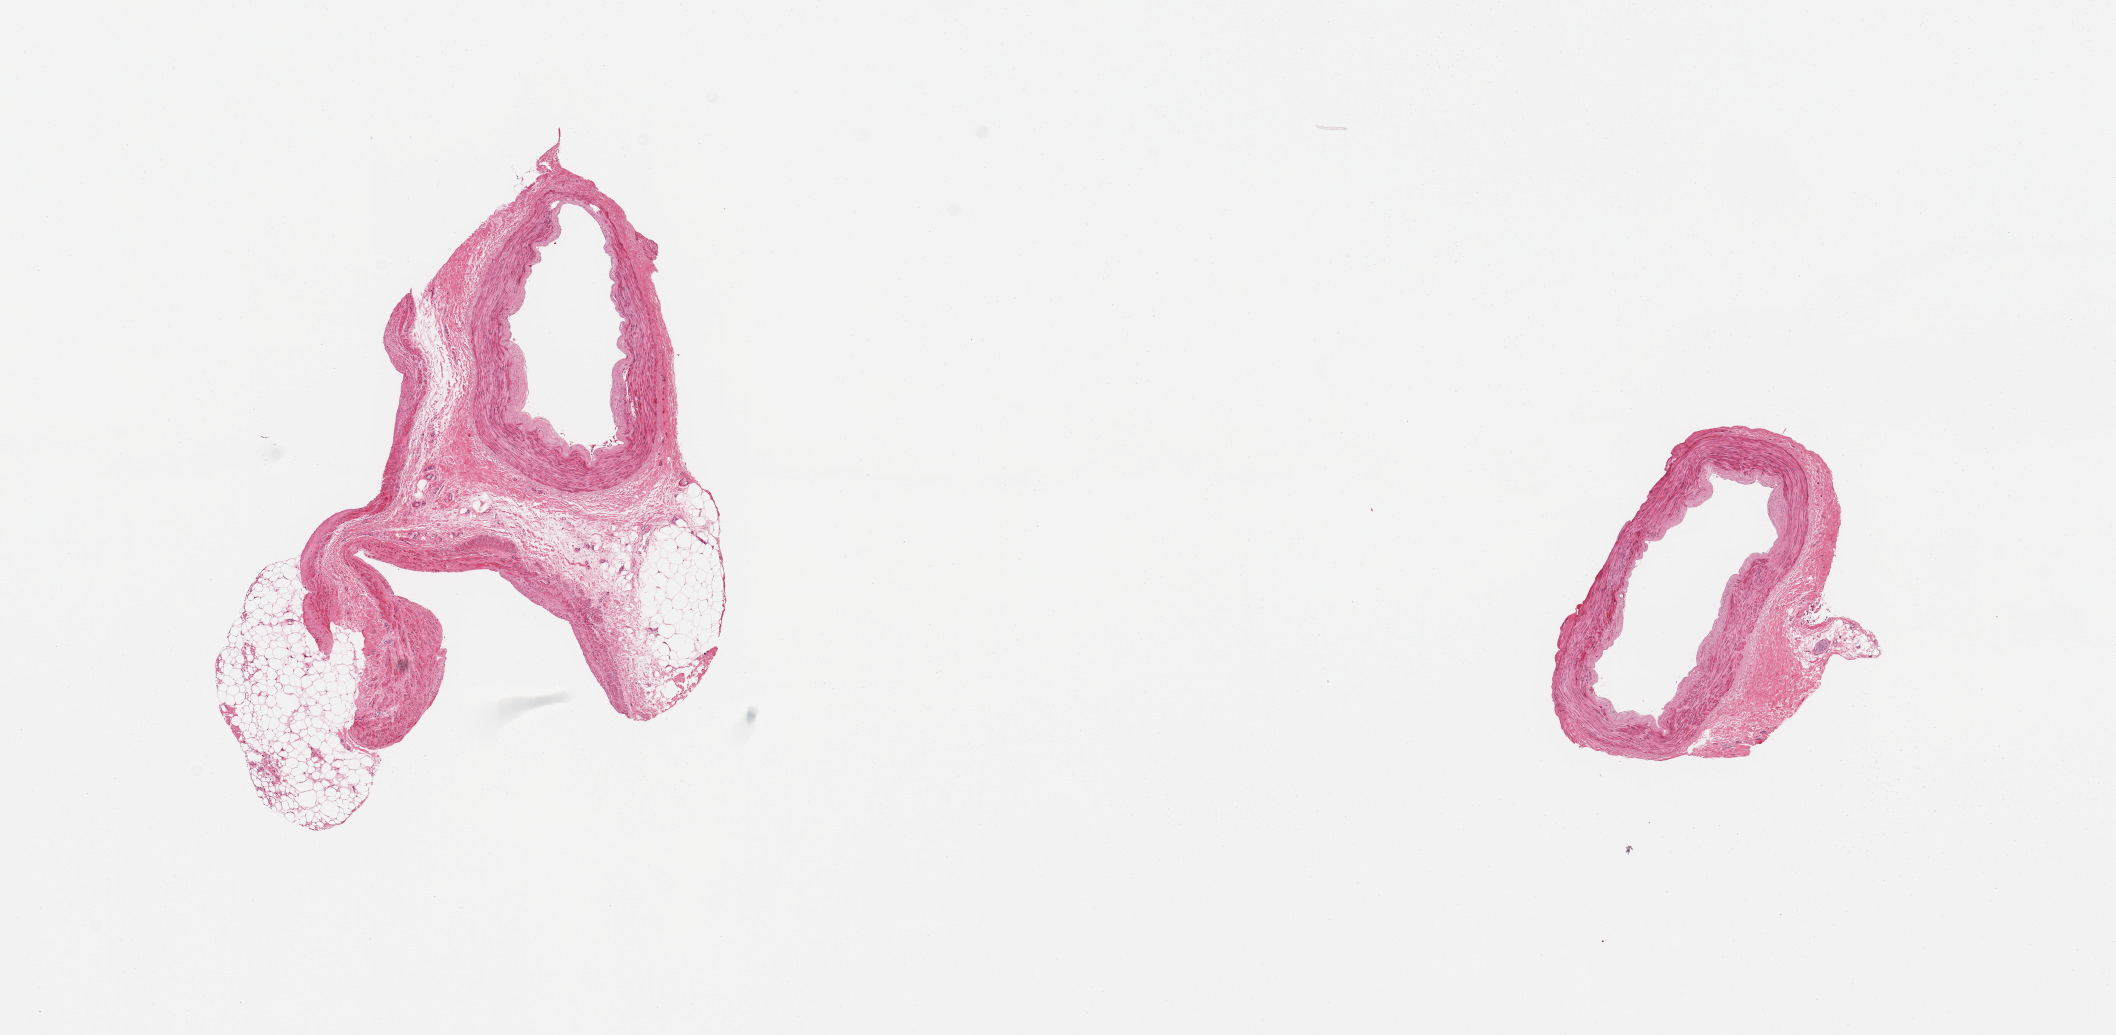
Digitized hematoxylin and eosin (H&E)-stained section — a low-resolution overview of the entire scanned area, about 16.7 x 8.2 mm (from a 20x scan), PAXgene-fixed, paraffin-embedded tissue, target tissue: tibial artery, donor tissue sample. Donor: male.
Review note (as recorded): 2 pieces, ~3x3mm nubbin aderent fibroadipose elements, one section.